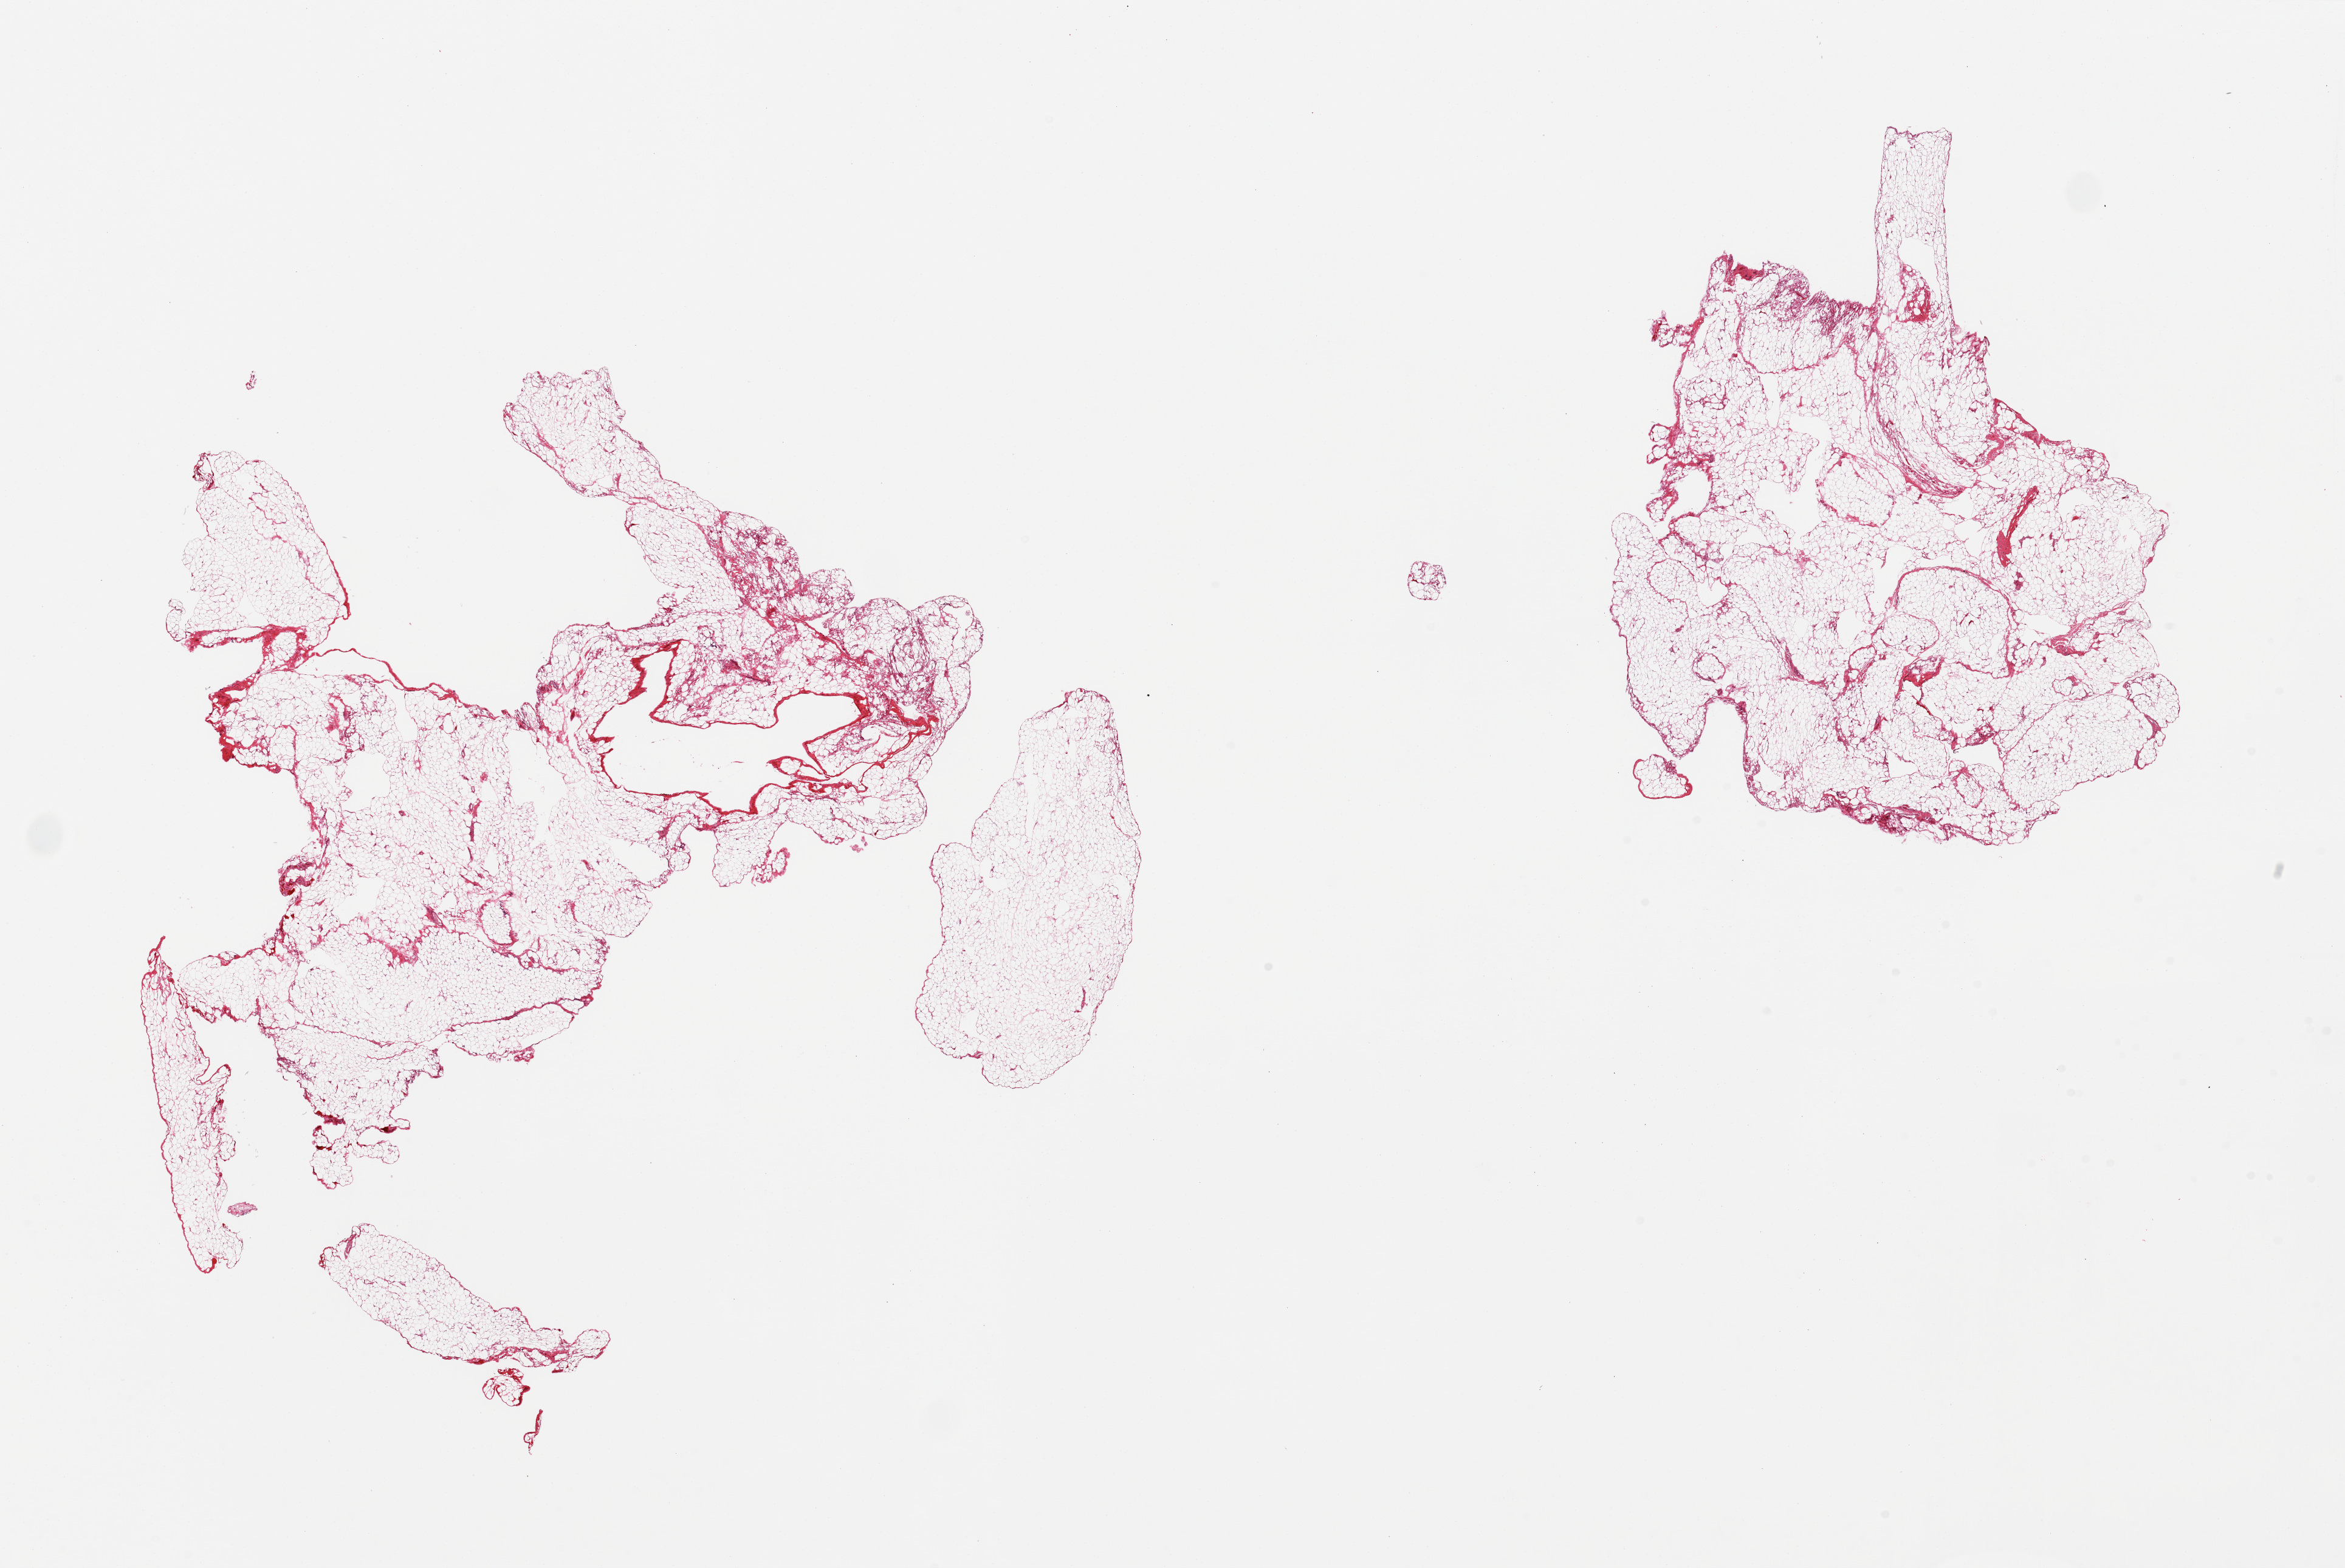
Digitized hematoxylin and eosin (H&E)-stained section, brightfield — low-resolution overview of the scanned area, about 30.5 x 20.4 mm (from a 20x scan). PAXgene-fixed paraffin-embedded (PFPE) section. Sampled site (target tissue): omentum. Donor tissue sample. Male donor.
Review note (as recorded): 2 pieces.